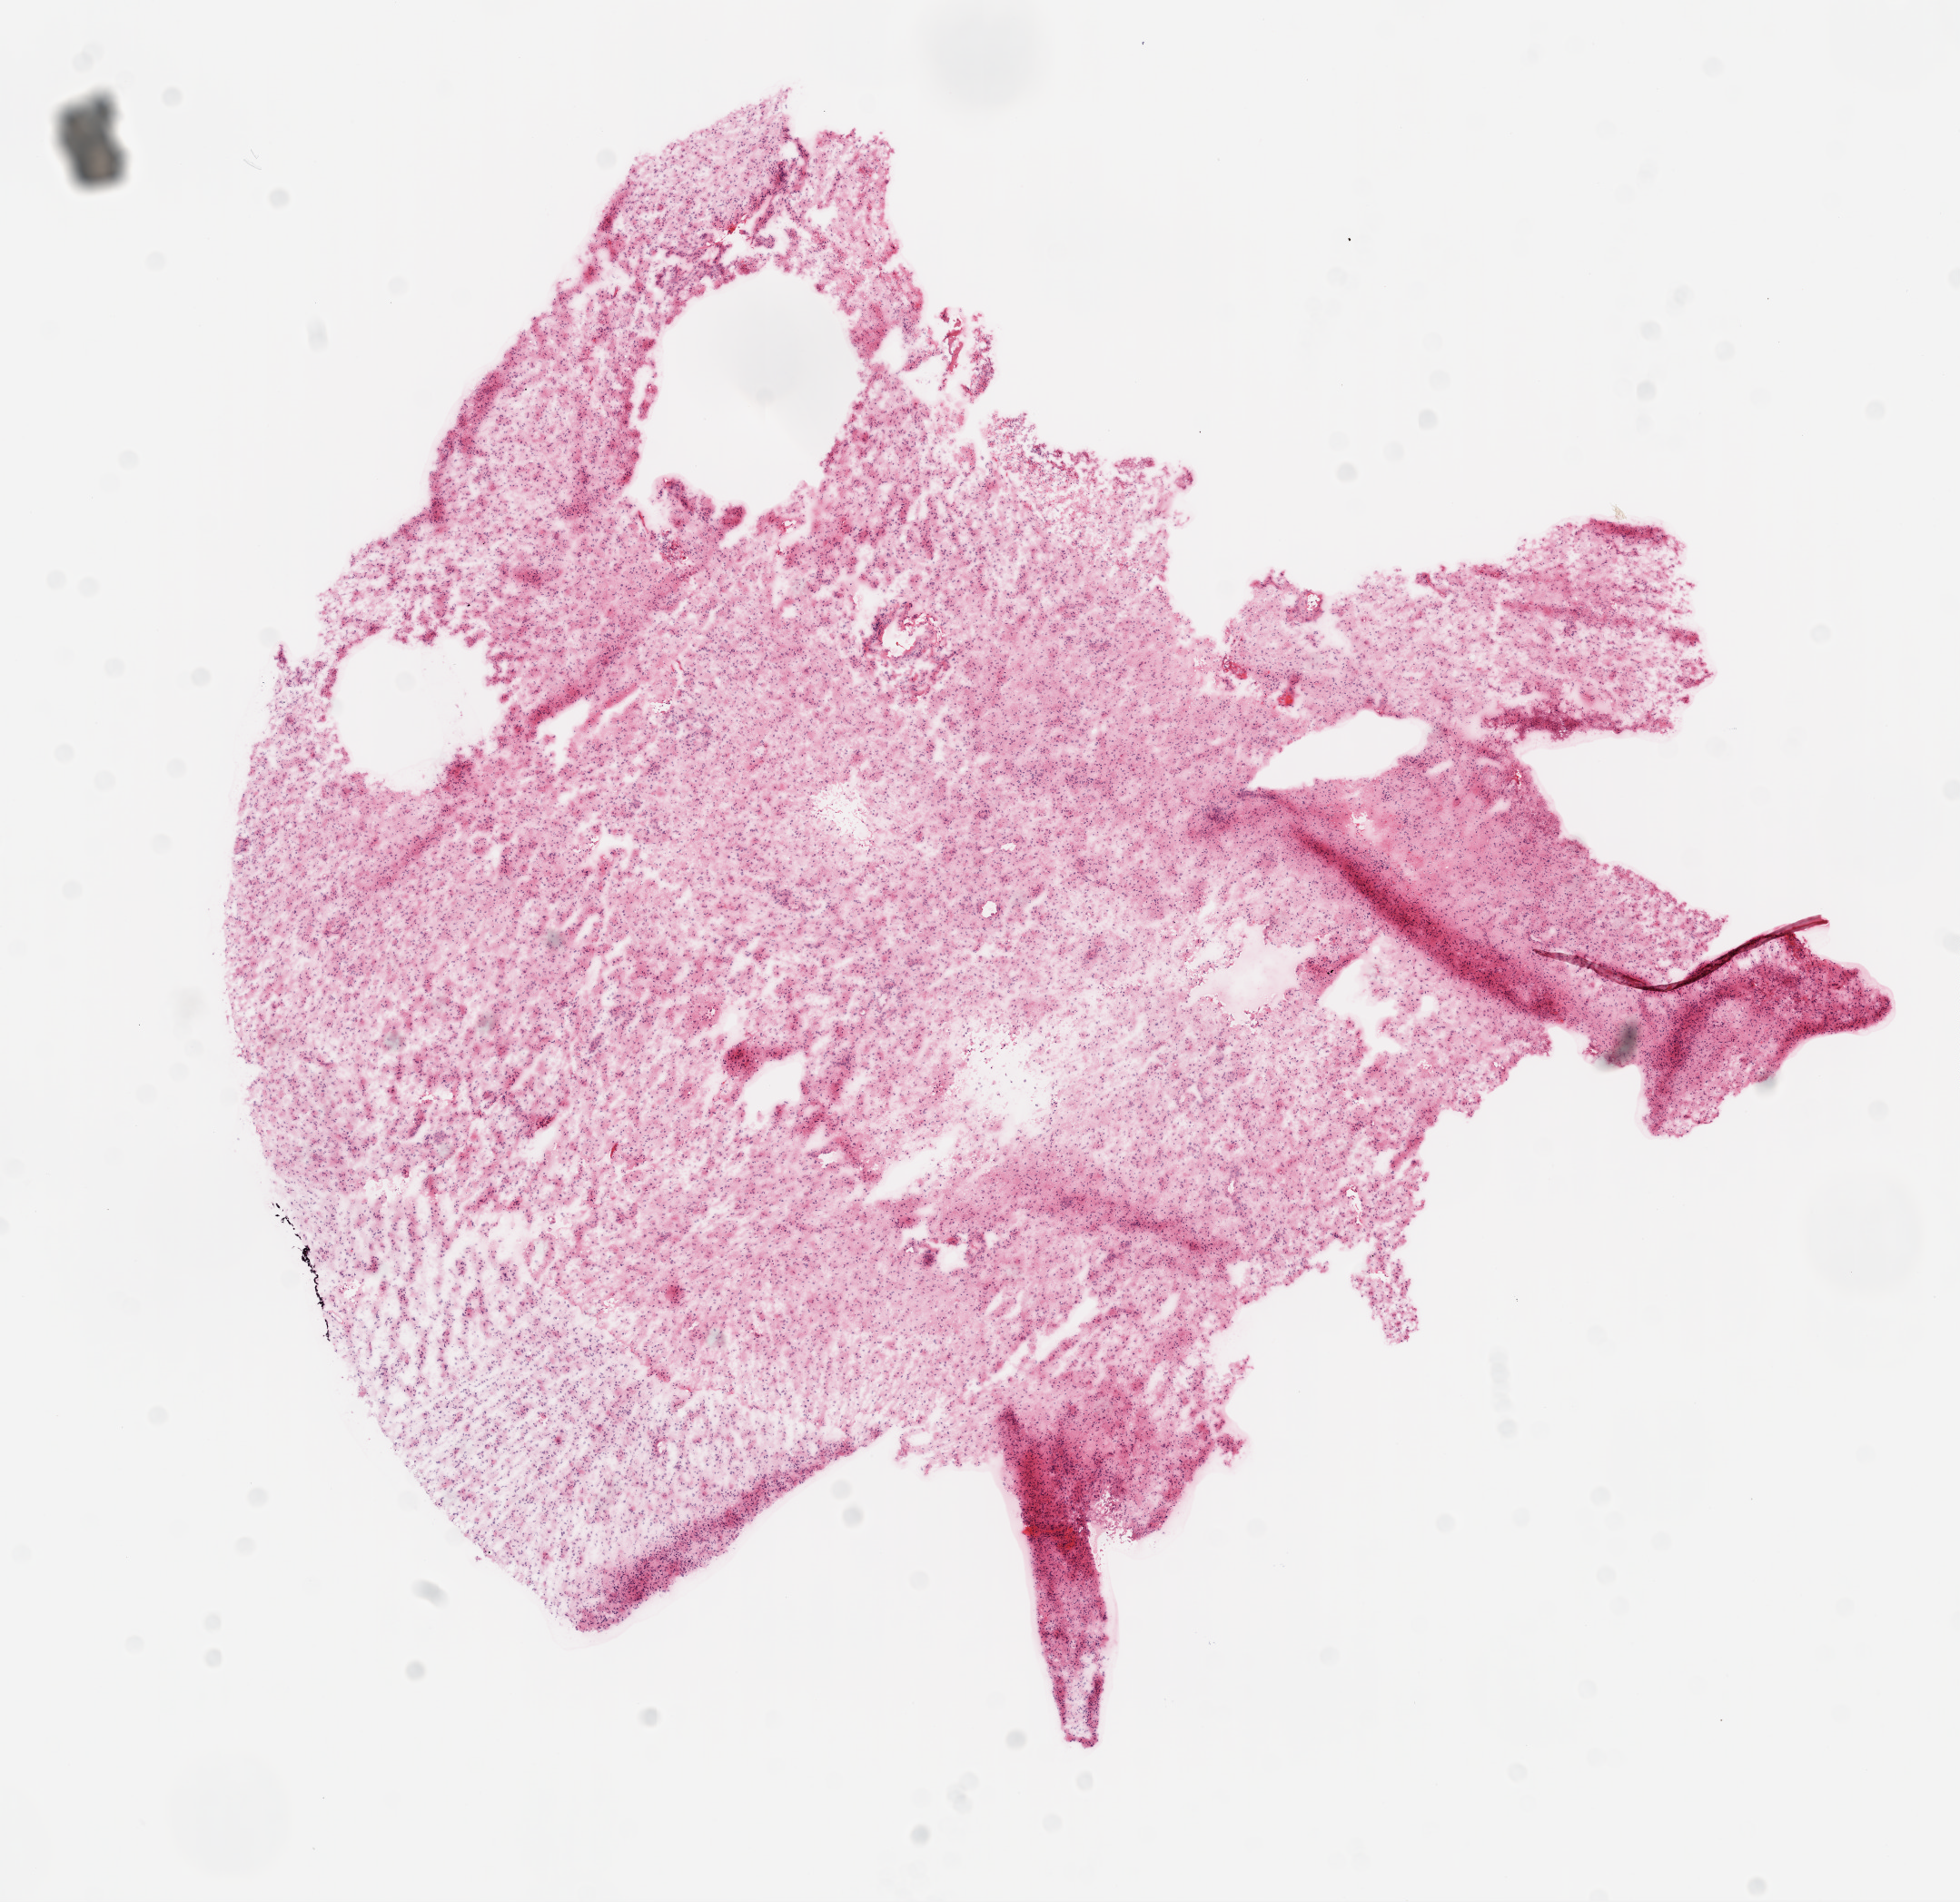
Digitized H&E-stained tissue section (whole slide), shown as a low-resolution overview of the whole scanned area (about 8.7 x 8.4 mm), frozen section from the top of the tissue portion, sample: primary tumour, brain. Female, age 71 years at initial diagnosis. Composition of this section per pathologist review: tumour cells 75%, tumour nuclei 85%, normal cells 0%, stromal cells 25%, necrosis 0%.
Diagnosis: Glioblastoma.